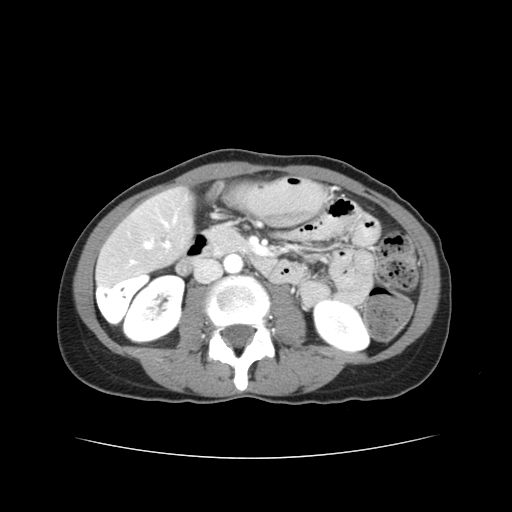
Contrast-enhanced abdominal CT, one axial slice. Reconstruction kernel STANDARD. Soft-tissue window (W 400 / L 40 HU). 512 × 512 image matrix. Female patient, age 54 years. From the clinical record (not read from this slice): diagnosis: colorectal cancer liver metastases, imaged before liver resection; multiple liver metastases: yes; largest metastasis: 1.1 cm; disease in both lobes: yes.
Annotated regions visible in this slice (expert manual segmentation):
- hepatic veins: bounding box <145,243,151,248> (left, top, right, bottom; pixels)
- liver: <99,191,190,280>
- portal vein (with intrahepatic branches): <131,222,170,264>